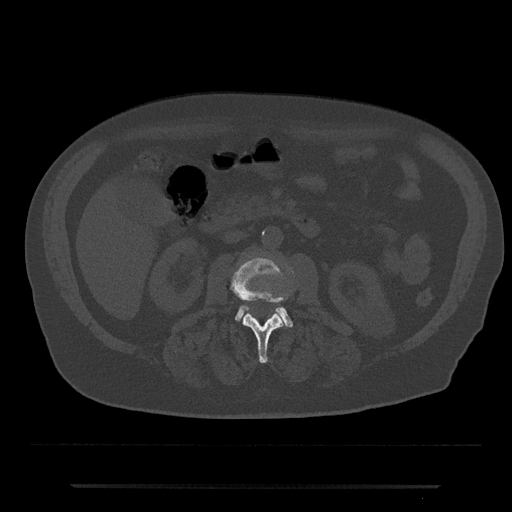
CT including the spine, one axial slice; slice 449 of 797 in the series (ordered by position); reconstruction kernel Br40s/3; bone window (W 1800 / L 400 HU); 512 × 512 image matrix, field of view 434 × 434 mm. Male patient, age 80 years. Case-level facts recorded for this patient, not image findings: primary cancer: prostate; vertebrae with lytic lesions (as recorded): L1, T11.
Structures marked on this image (semi-automatically segmented with operator editing):
- L2 vertebra: box from (x=231, y=258) to (x=288, y=363) px
- L3 vertebra: (x=235, y=305)–(x=293, y=327)